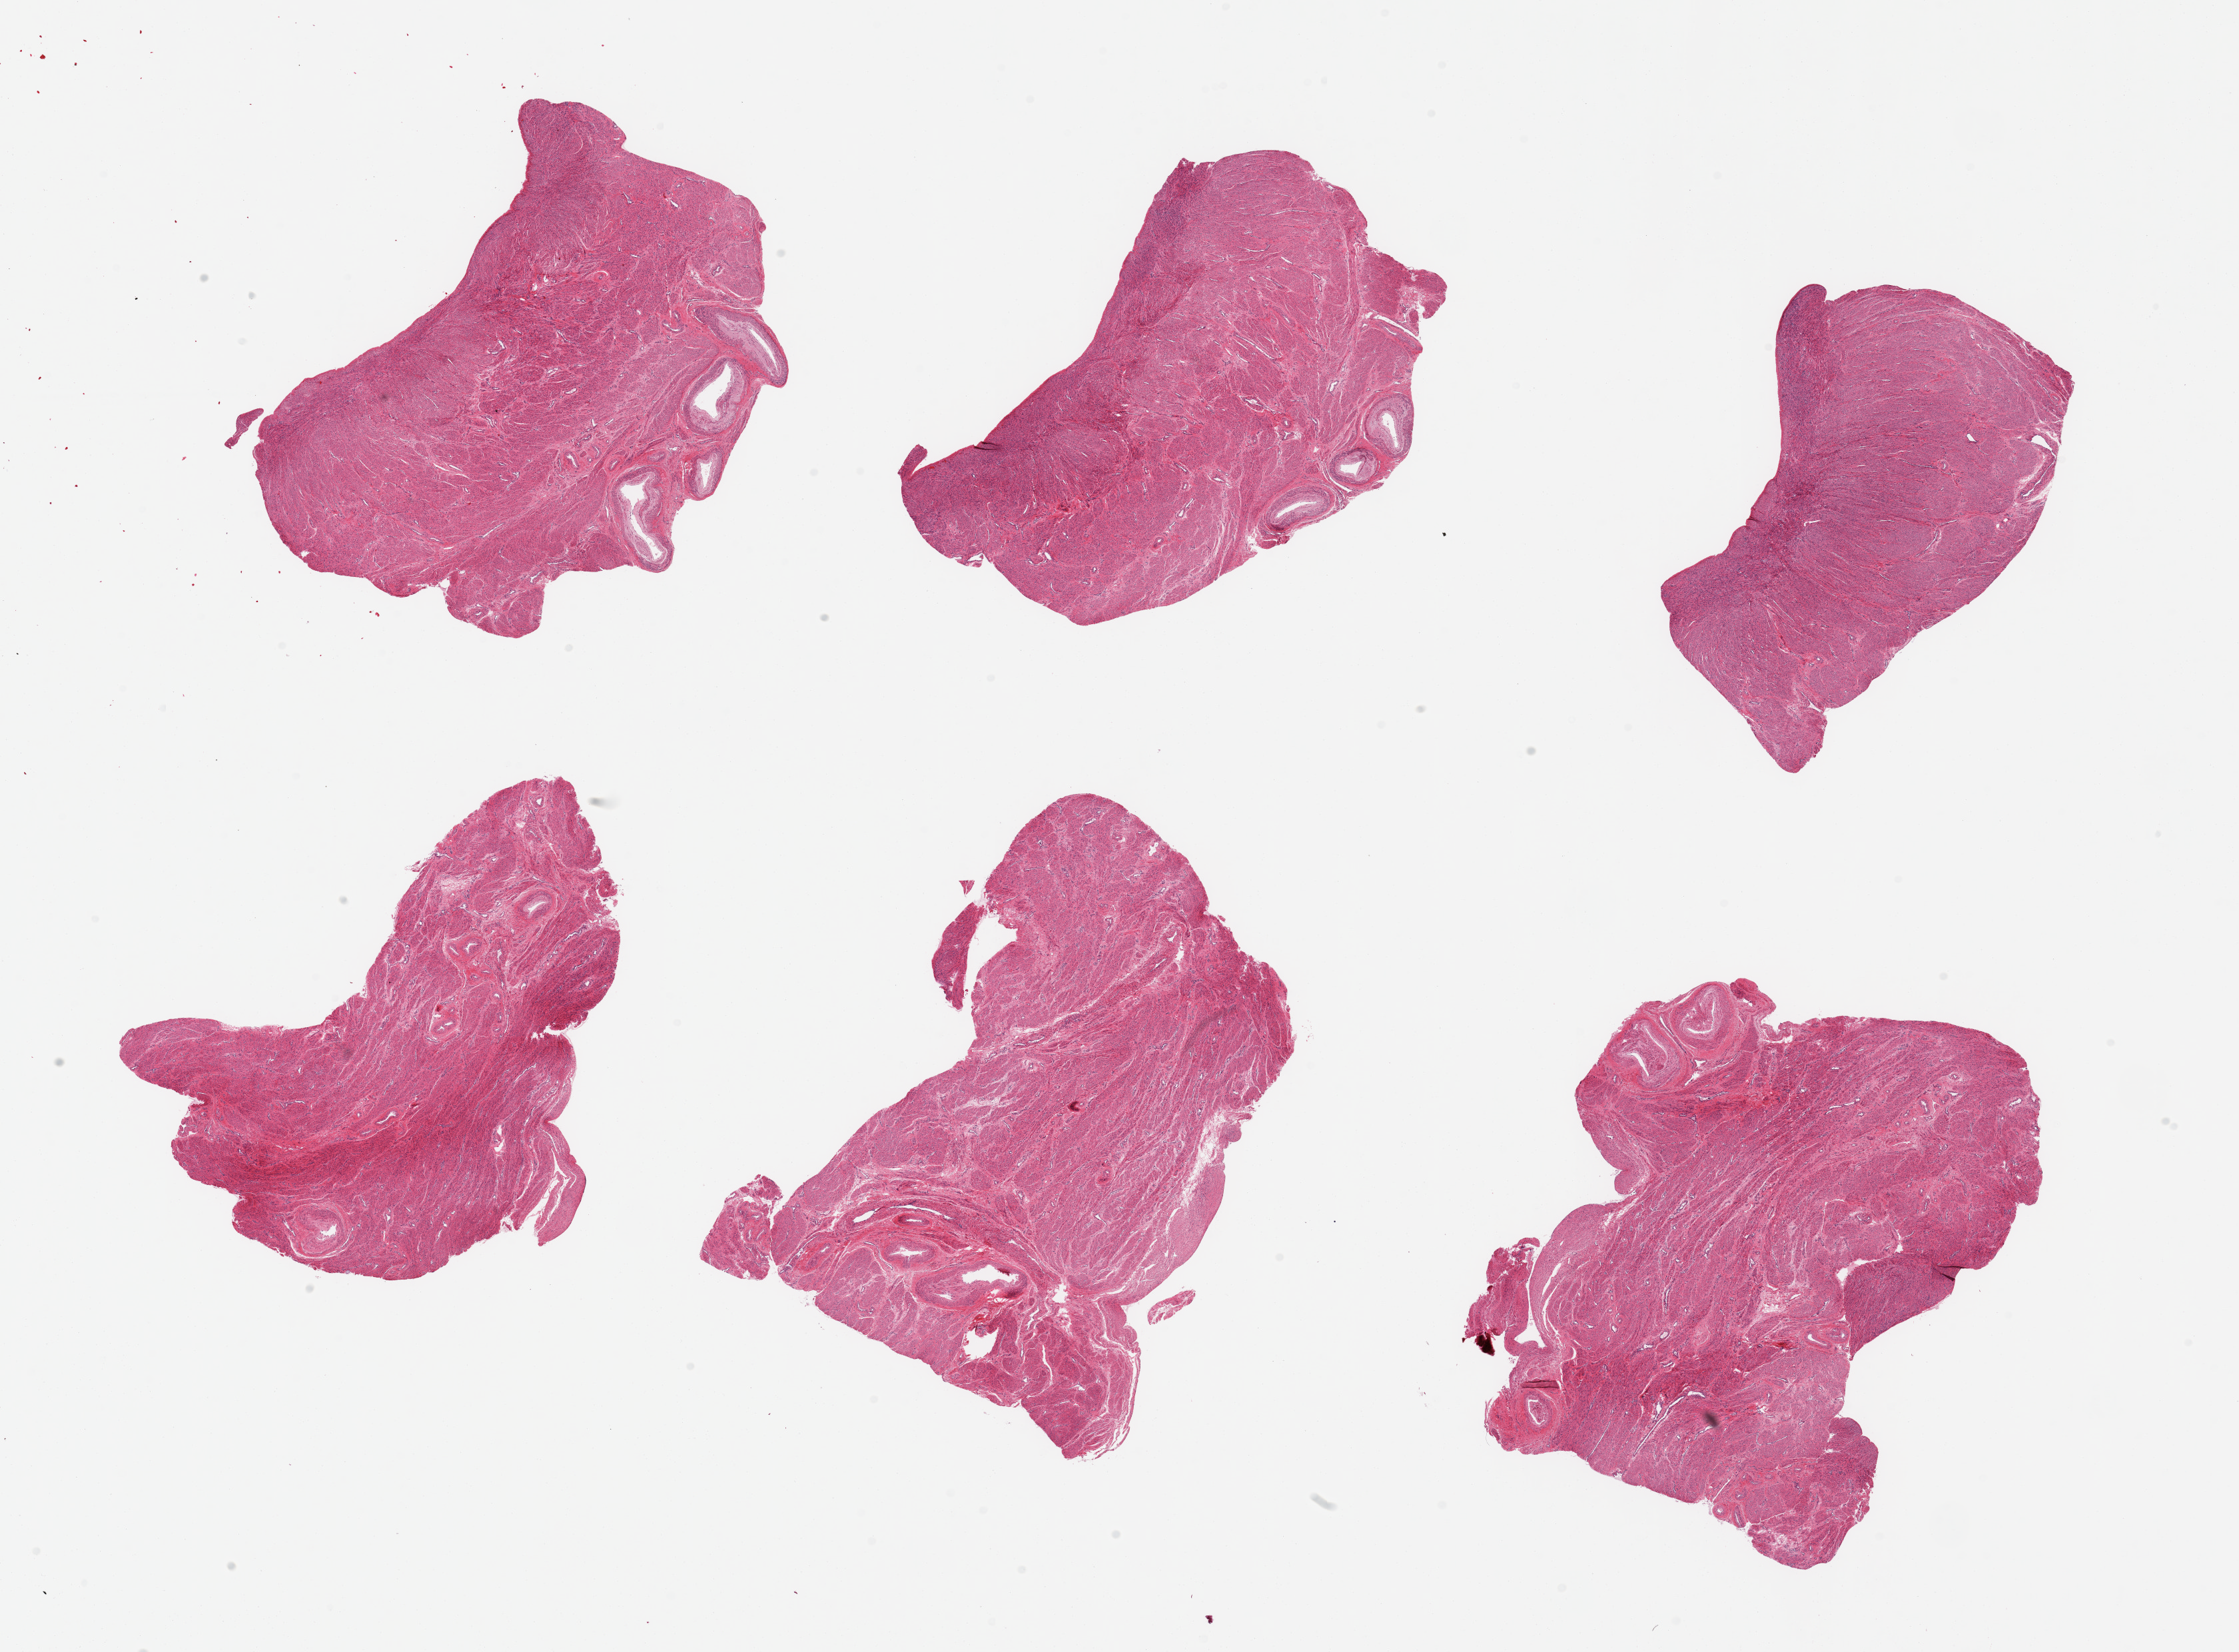
Digitized hematoxylin and eosin (H&E)-stained section, shown as a low-resolution overview of the whole scanned area (about 26.6 x 19.6 mm, slide scanned at 20x). PAXgene-fixed, paraffin-embedded tissue. Section of vagina (target tissue). Donor tissue sample.
* reviewer comment on this tissue sample: 6 pieces; uterus (lower segment) sampled not vagina